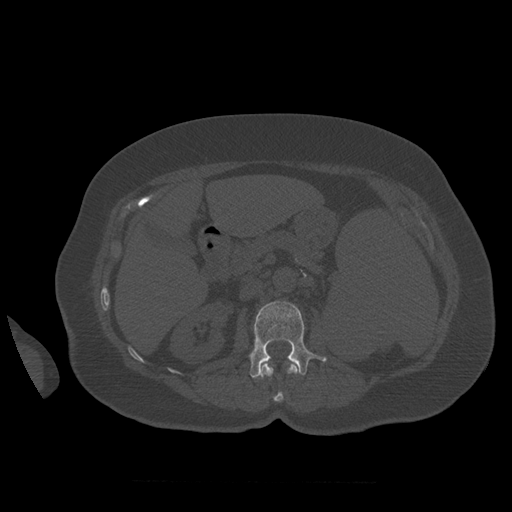
CT including the spine, one axial slice; slice 260 of 399 in the series (ordered by position); reconstruction kernel STANDARD; bone window (W 1800 / L 400 HU); 512 × 512 image matrix, field of view 404 × 404 mm. Patient age 81 years. Case-level facts recorded for this patient, not image findings: primary cancer: renal.
Outlined on this slice (semi-automatic segmentation, software-assisted and operator-edited):
- L1 vertebra: bounding box [x1, y1, x2, y2] px = [260, 363, 298, 402]
- L2 vertebra: [249, 301, 327, 378]